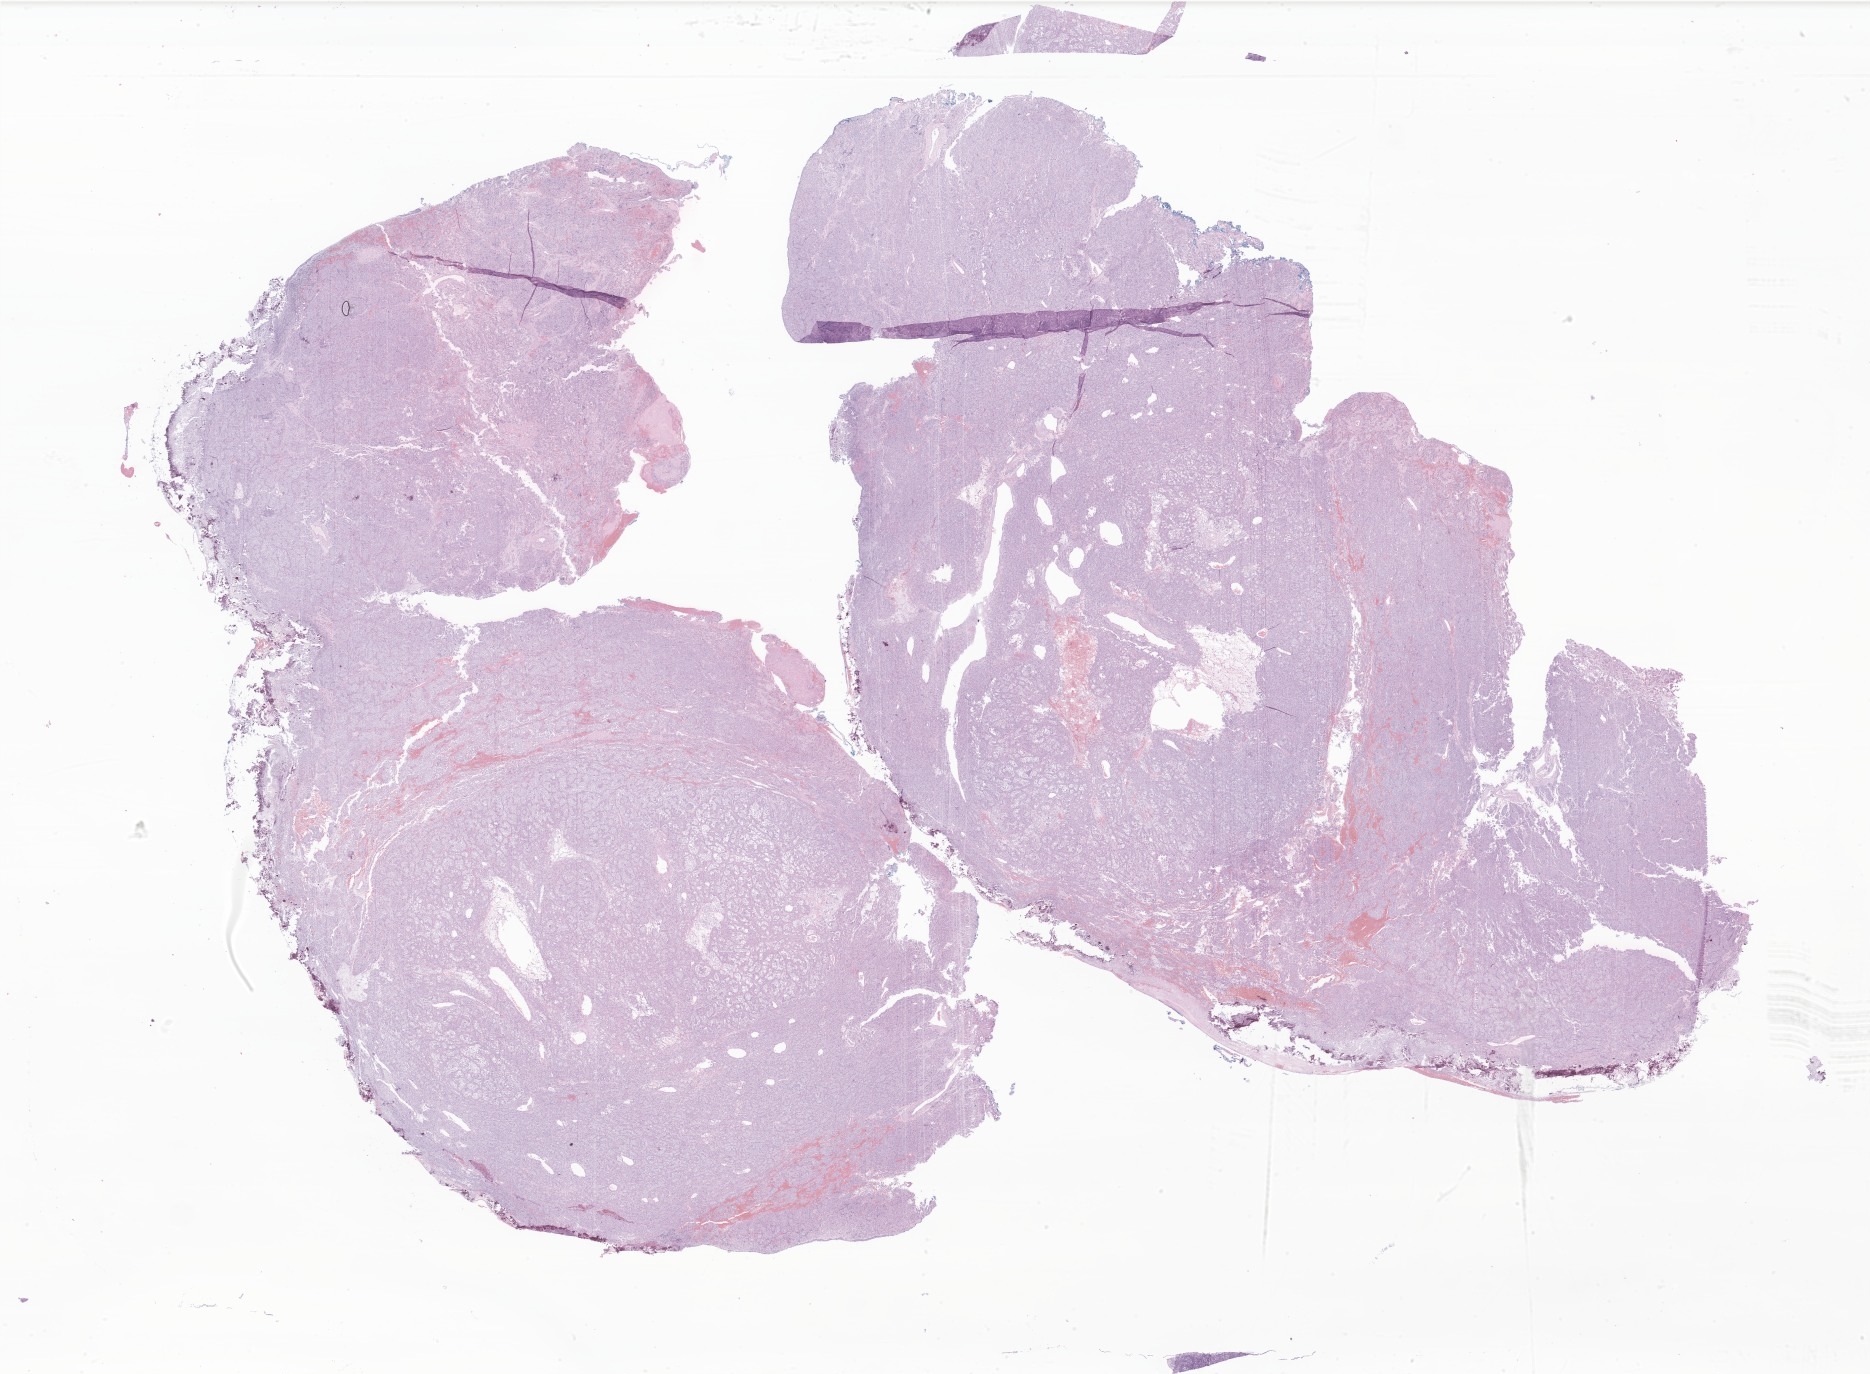
Digitized H&E-stained section of tumor tissue from the urinary bladder — low-resolution overview of the scanned area, about 31.5 x 23.2 mm, formalin-fixed, paraffin-embedded (FFPE) tissue. Patient female; age 189 months (15 years 9 months).
- diagnosis (ICD-O-3 morphology term): Epithelioid sarcoma, NOS